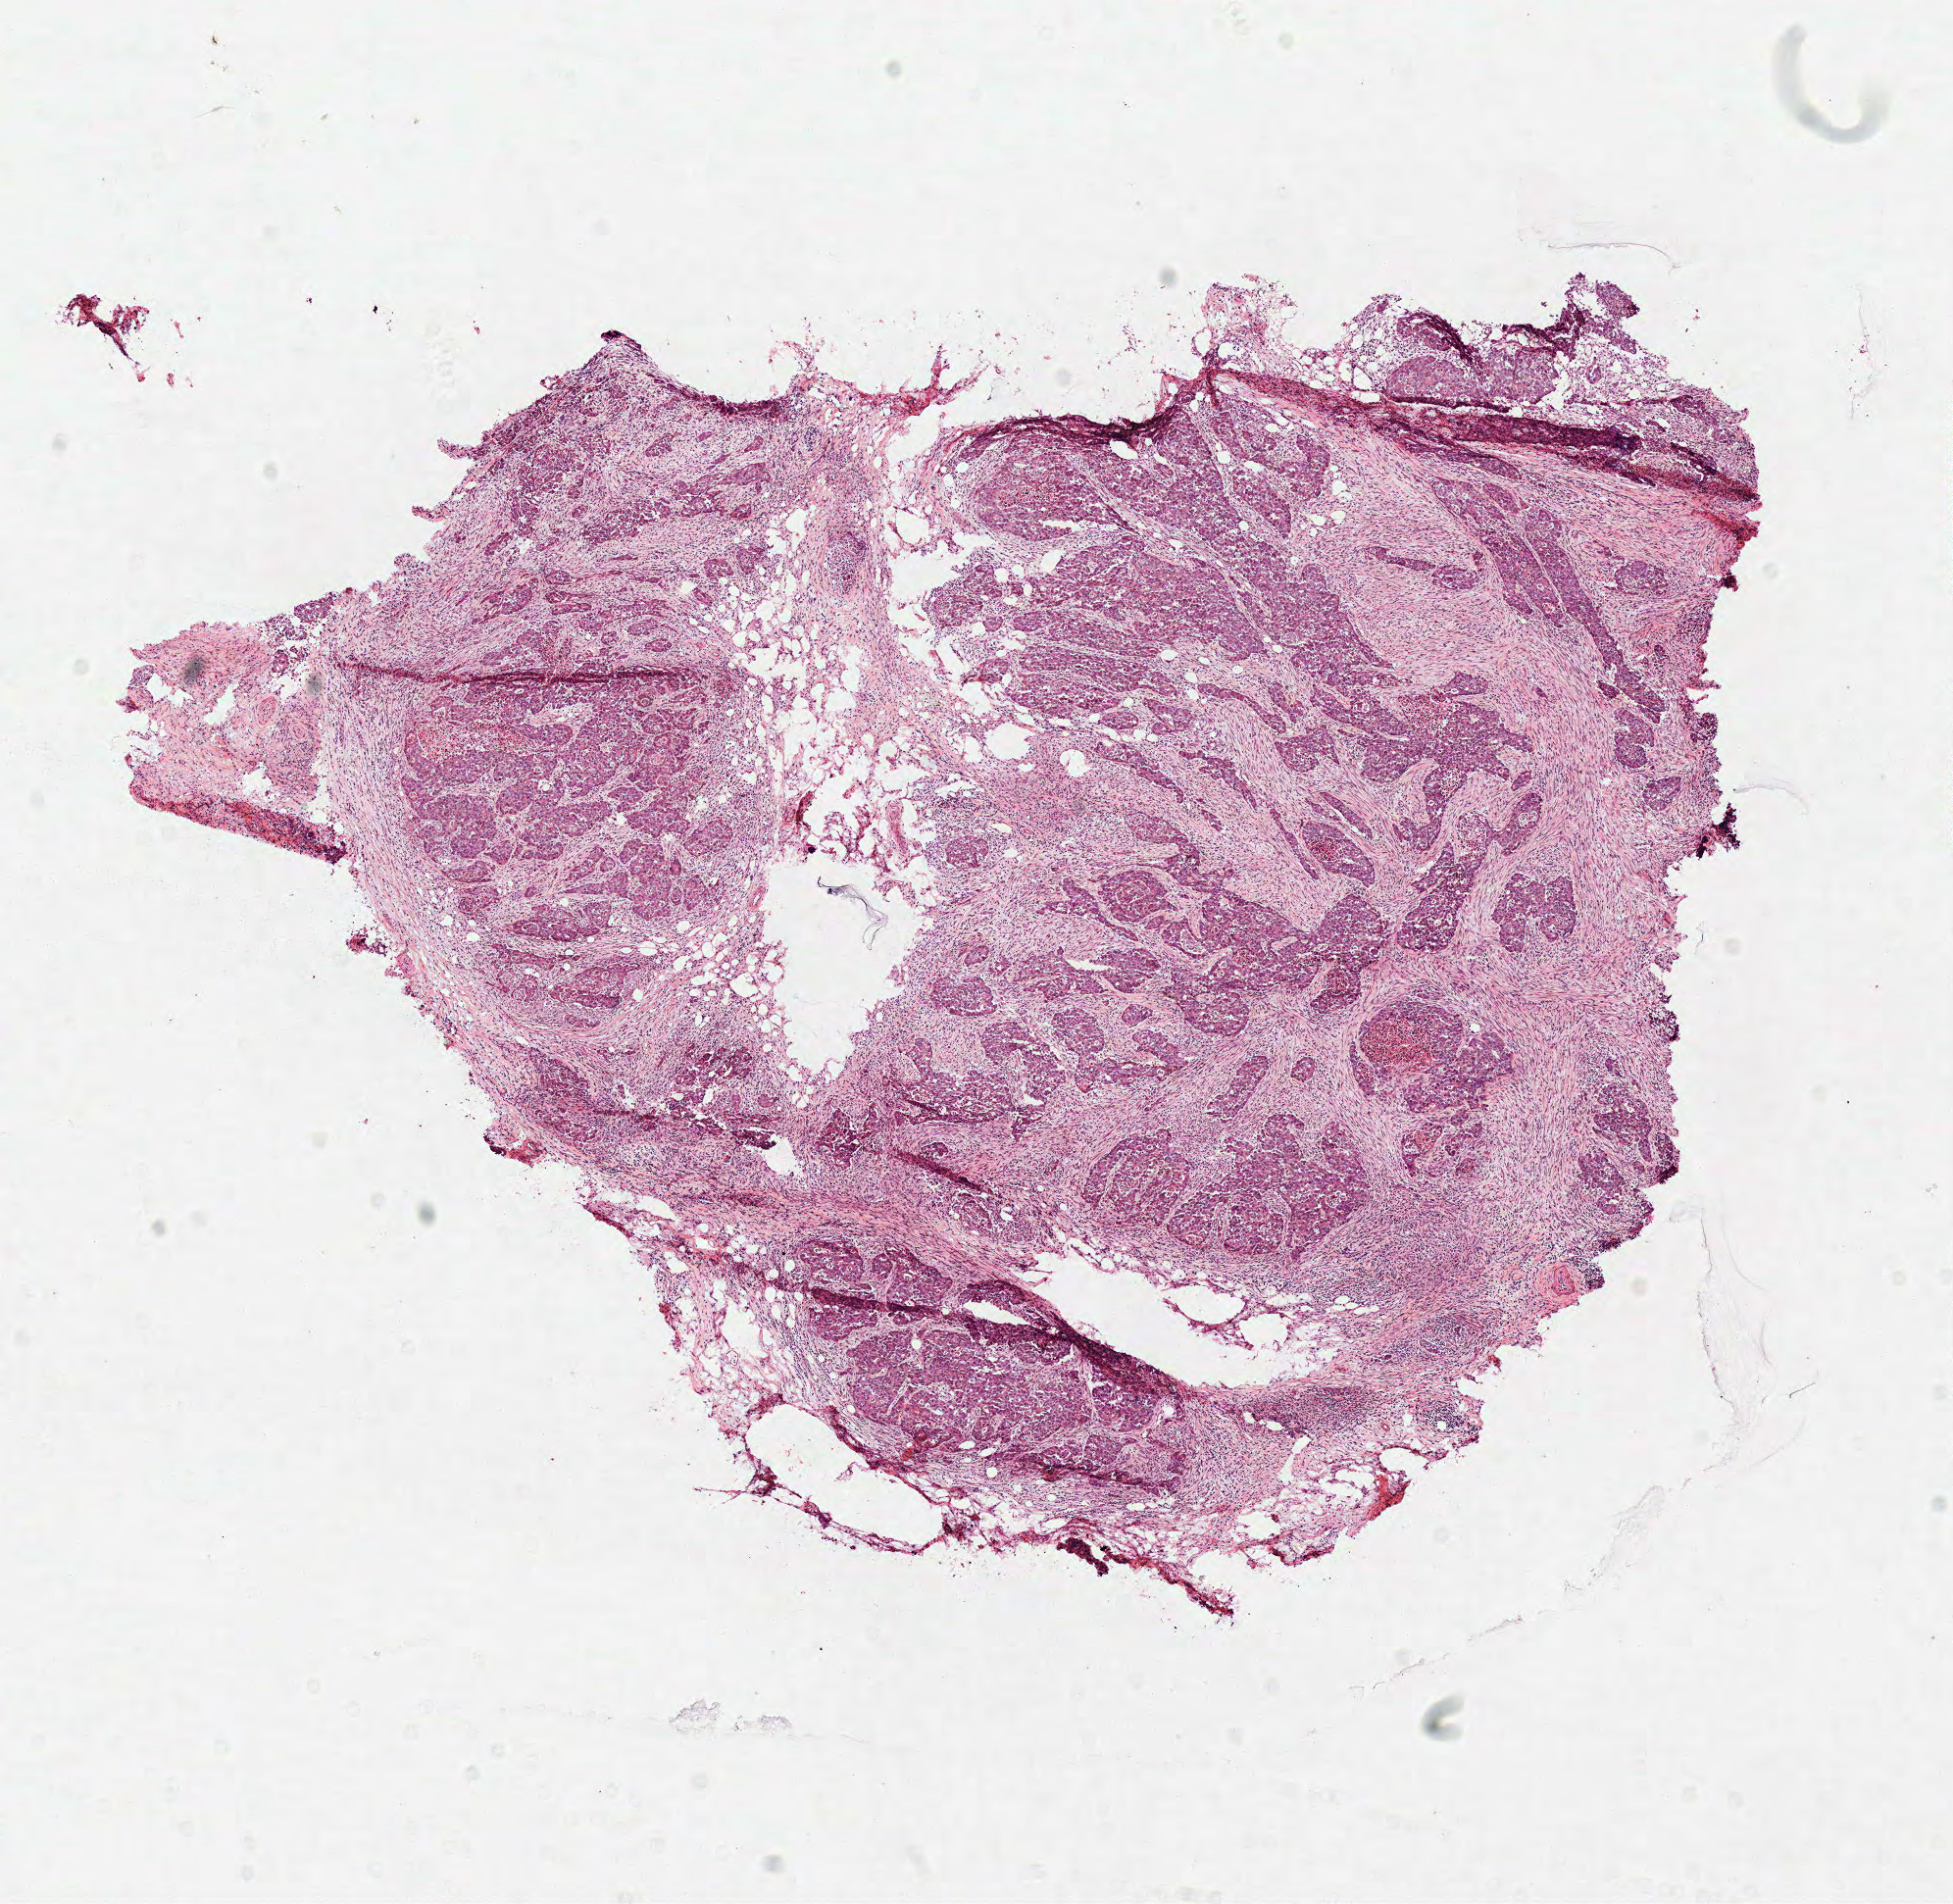
Digitized H&E tissue section (whole slide) — a low-resolution overview of the entire scanned area, about 7.8 x 7.6 mm, frozen section, primary tumour sample from the colon. Male patient; age at initial diagnosis 69 years.
Histologic diagnosis: Adenocarcinoma, NOS (descending colon).